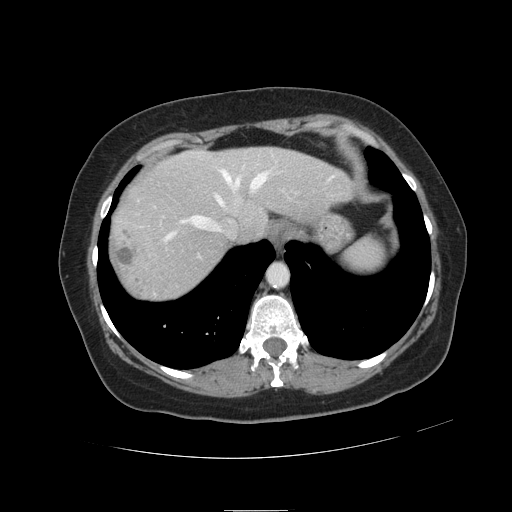
Contrast-enhanced abdominal CT, one axial slice. Position 99 of 121 along the scan axis. Intravenous contrast given. Soft-tissue window (W 400 / L 40 HU). 2.5 mm slice thickness. 512 × 512 image matrix, field of view 400 × 400 mm. Female patient, age 52 years. Case-level facts recorded for this patient, not image findings: diagnosis: colorectal cancer liver metastases, imaged before liver resection; multiple liver metastases: yes; largest metastasis: 6.3 cm; disease in both lobes: no.
Annotated regions visible in this slice (outlined manually by an expert reader):
- hepatic veins: box from (x=165, y=170) to (x=267, y=240) px
- liver: (x=110, y=148)–(x=350, y=301)
- planned liver remnant (the part of the liver to remain after resection): (x=171, y=148)–(x=351, y=242)
- liver metastasis: (x=114, y=246)–(x=135, y=268)